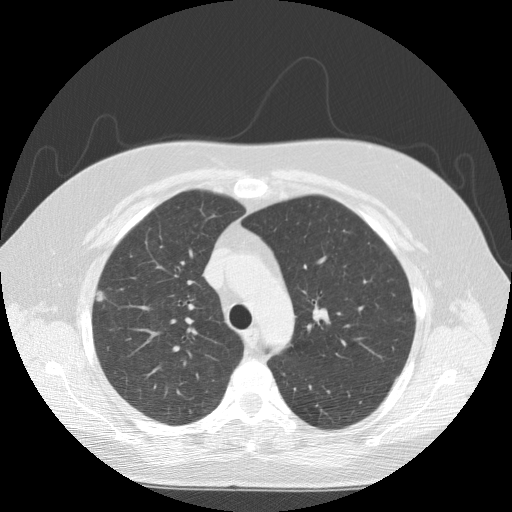
Low-dose screening chest CT, one axial slice; reconstruction kernel STANDARD; lung window (W 1500 / L -600 HU); 2.5 mm slice thickness; 512 × 512 image matrix, field of view 370 × 370 mm.
Structures marked on this image (expert manual segmentation):
- lesion 1 (tumor, upper lobe of right lung): bounding box (x1, y1, x2, y2) in pixels: (97, 291, 104, 301)